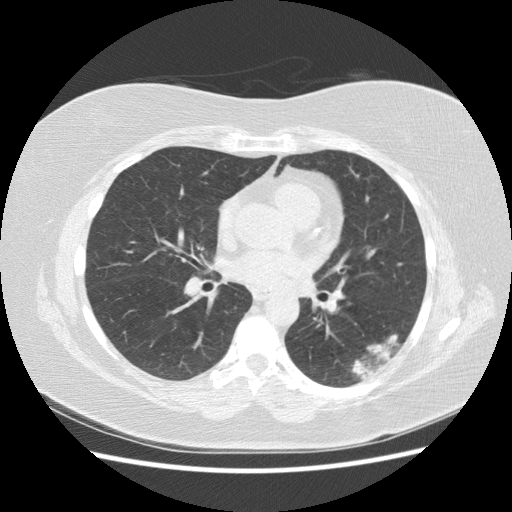
Low-dose screening chest CT, one axial slice. Slice 79 of 151 in the series (ordered by position). Reconstruction kernel STANDARD. 120 kVp. Lung window (W 1500 / L -600 HU). 2.5 mm slice thickness. 512 × 512 image matrix, field of view 360 × 360 mm.
Outlined on this slice (manually delineated by an expert):
- lesion 1 (tumor, lower lobe of left lung): bounding box [x1, y1, x2, y2] px = [352, 334, 400, 380]